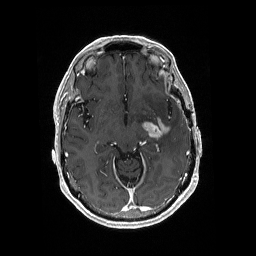
Brain MRI from a brain-tumour surgery series, one axial slice; position 109 of 176 along the scan axis; T1-weighted post-contrast; 256 × 256 image matrix, field of view 256 × 256 mm. Case-level facts recorded for this patient, not image findings: histopathology: Glioblastoma; WHO grade: 4; IDH mutation: no.
Annotated regions visible in this slice (outlined manually by an expert reader):
- tumour: bounding box <141,118,171,140> (left, top, right, bottom; pixels)